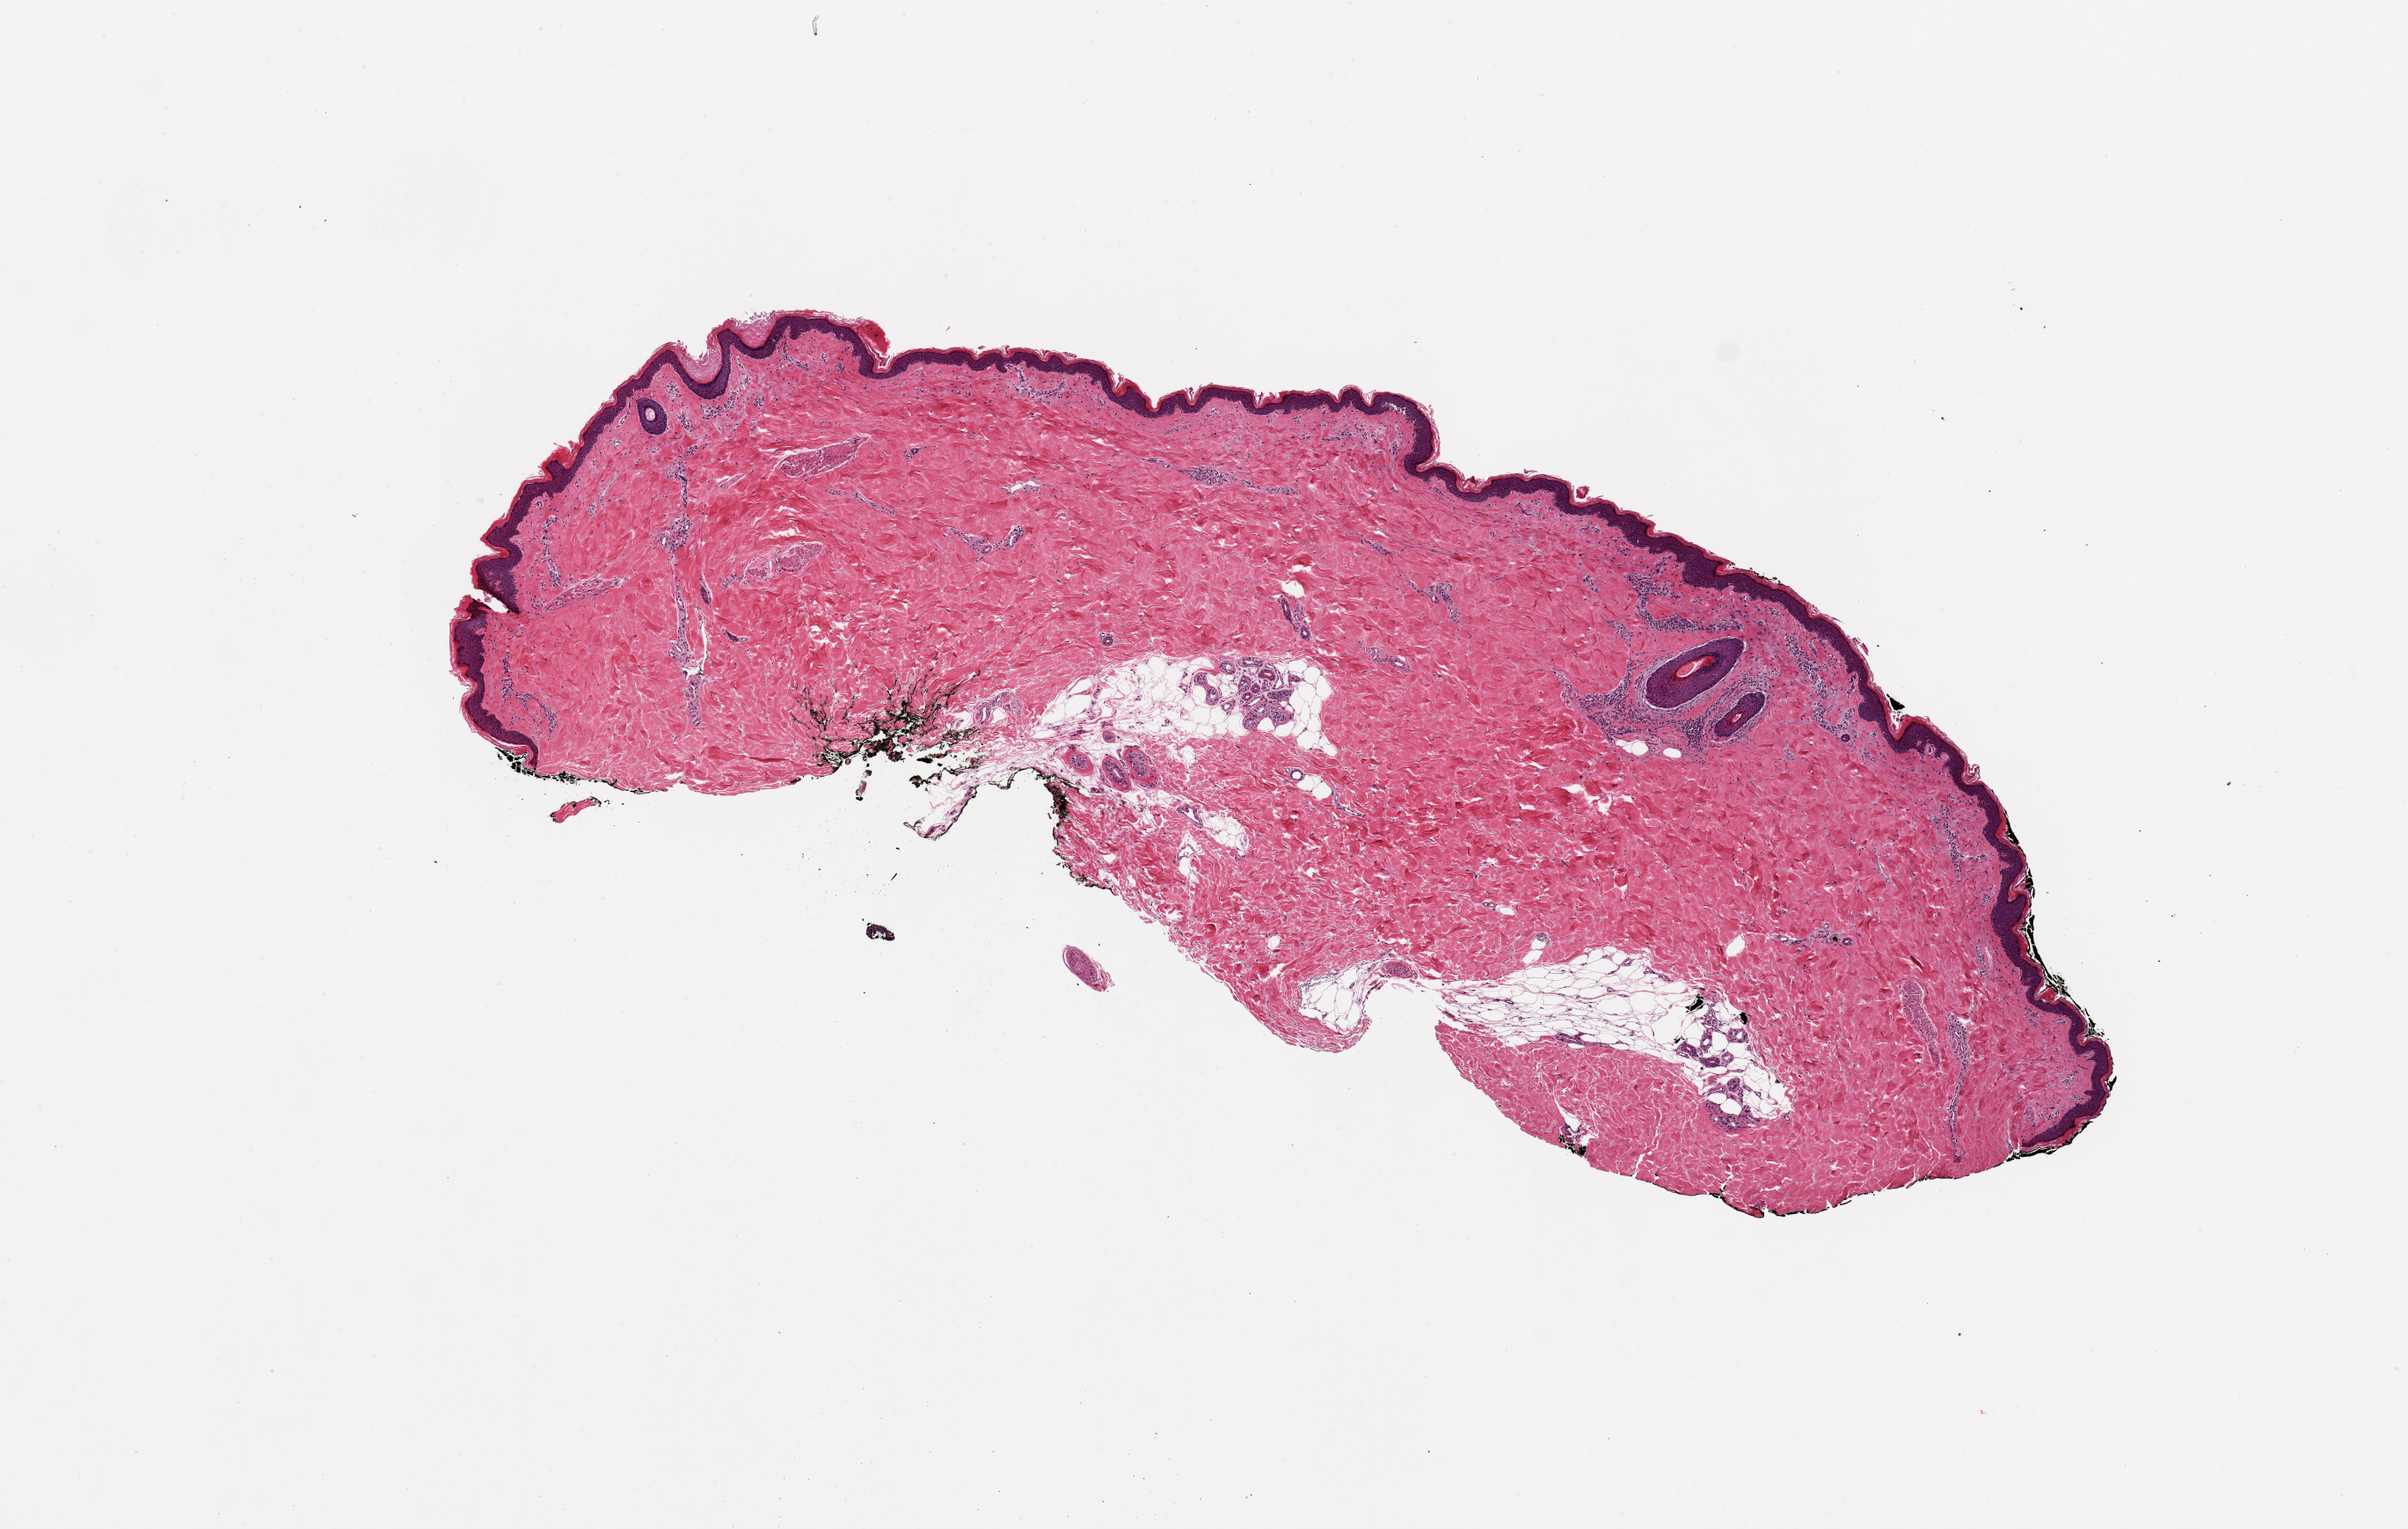
Digitized haematoxylin and eosin-stained section, low-resolution overview of the scanned area, about 10.8 x 6.9 mm; PAXgene-fixed paraffin-embedded (PFPE) section; section of skin of lower leg (target tissue); donor tissue sample. Donor sex: male.
* review note (as recorded): 1 piece (8x3mm), correlates with2125